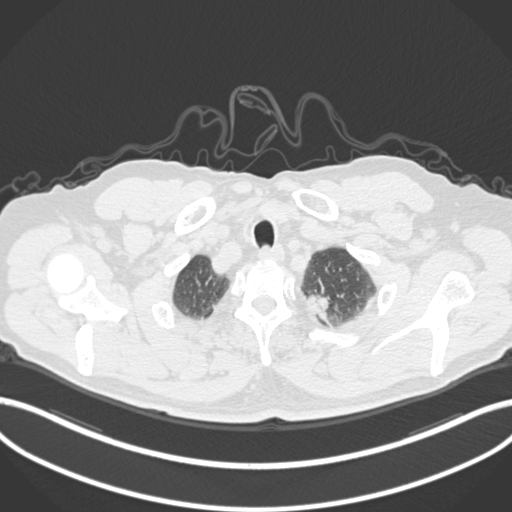
Chest CT, one axial slice. Slice 293 of 306 in the series (ordered by position). 120 kVp. Lung window (W 1500 / L -600 HU). 1 mm slice thickness. 512 × 512 image matrix, field of view 400 × 400 mm. Male patient, age 64 years. From the clinical record (not read from this slice): clinical TNM (as recorded): T1c N0 M0.
Outlined on this slice (bounding box drawn by a radiologist):
- lung tumour (recorded histology: adenocarcinoma): bounding box [x1, y1, x2, y2] px = [301, 286, 335, 319]